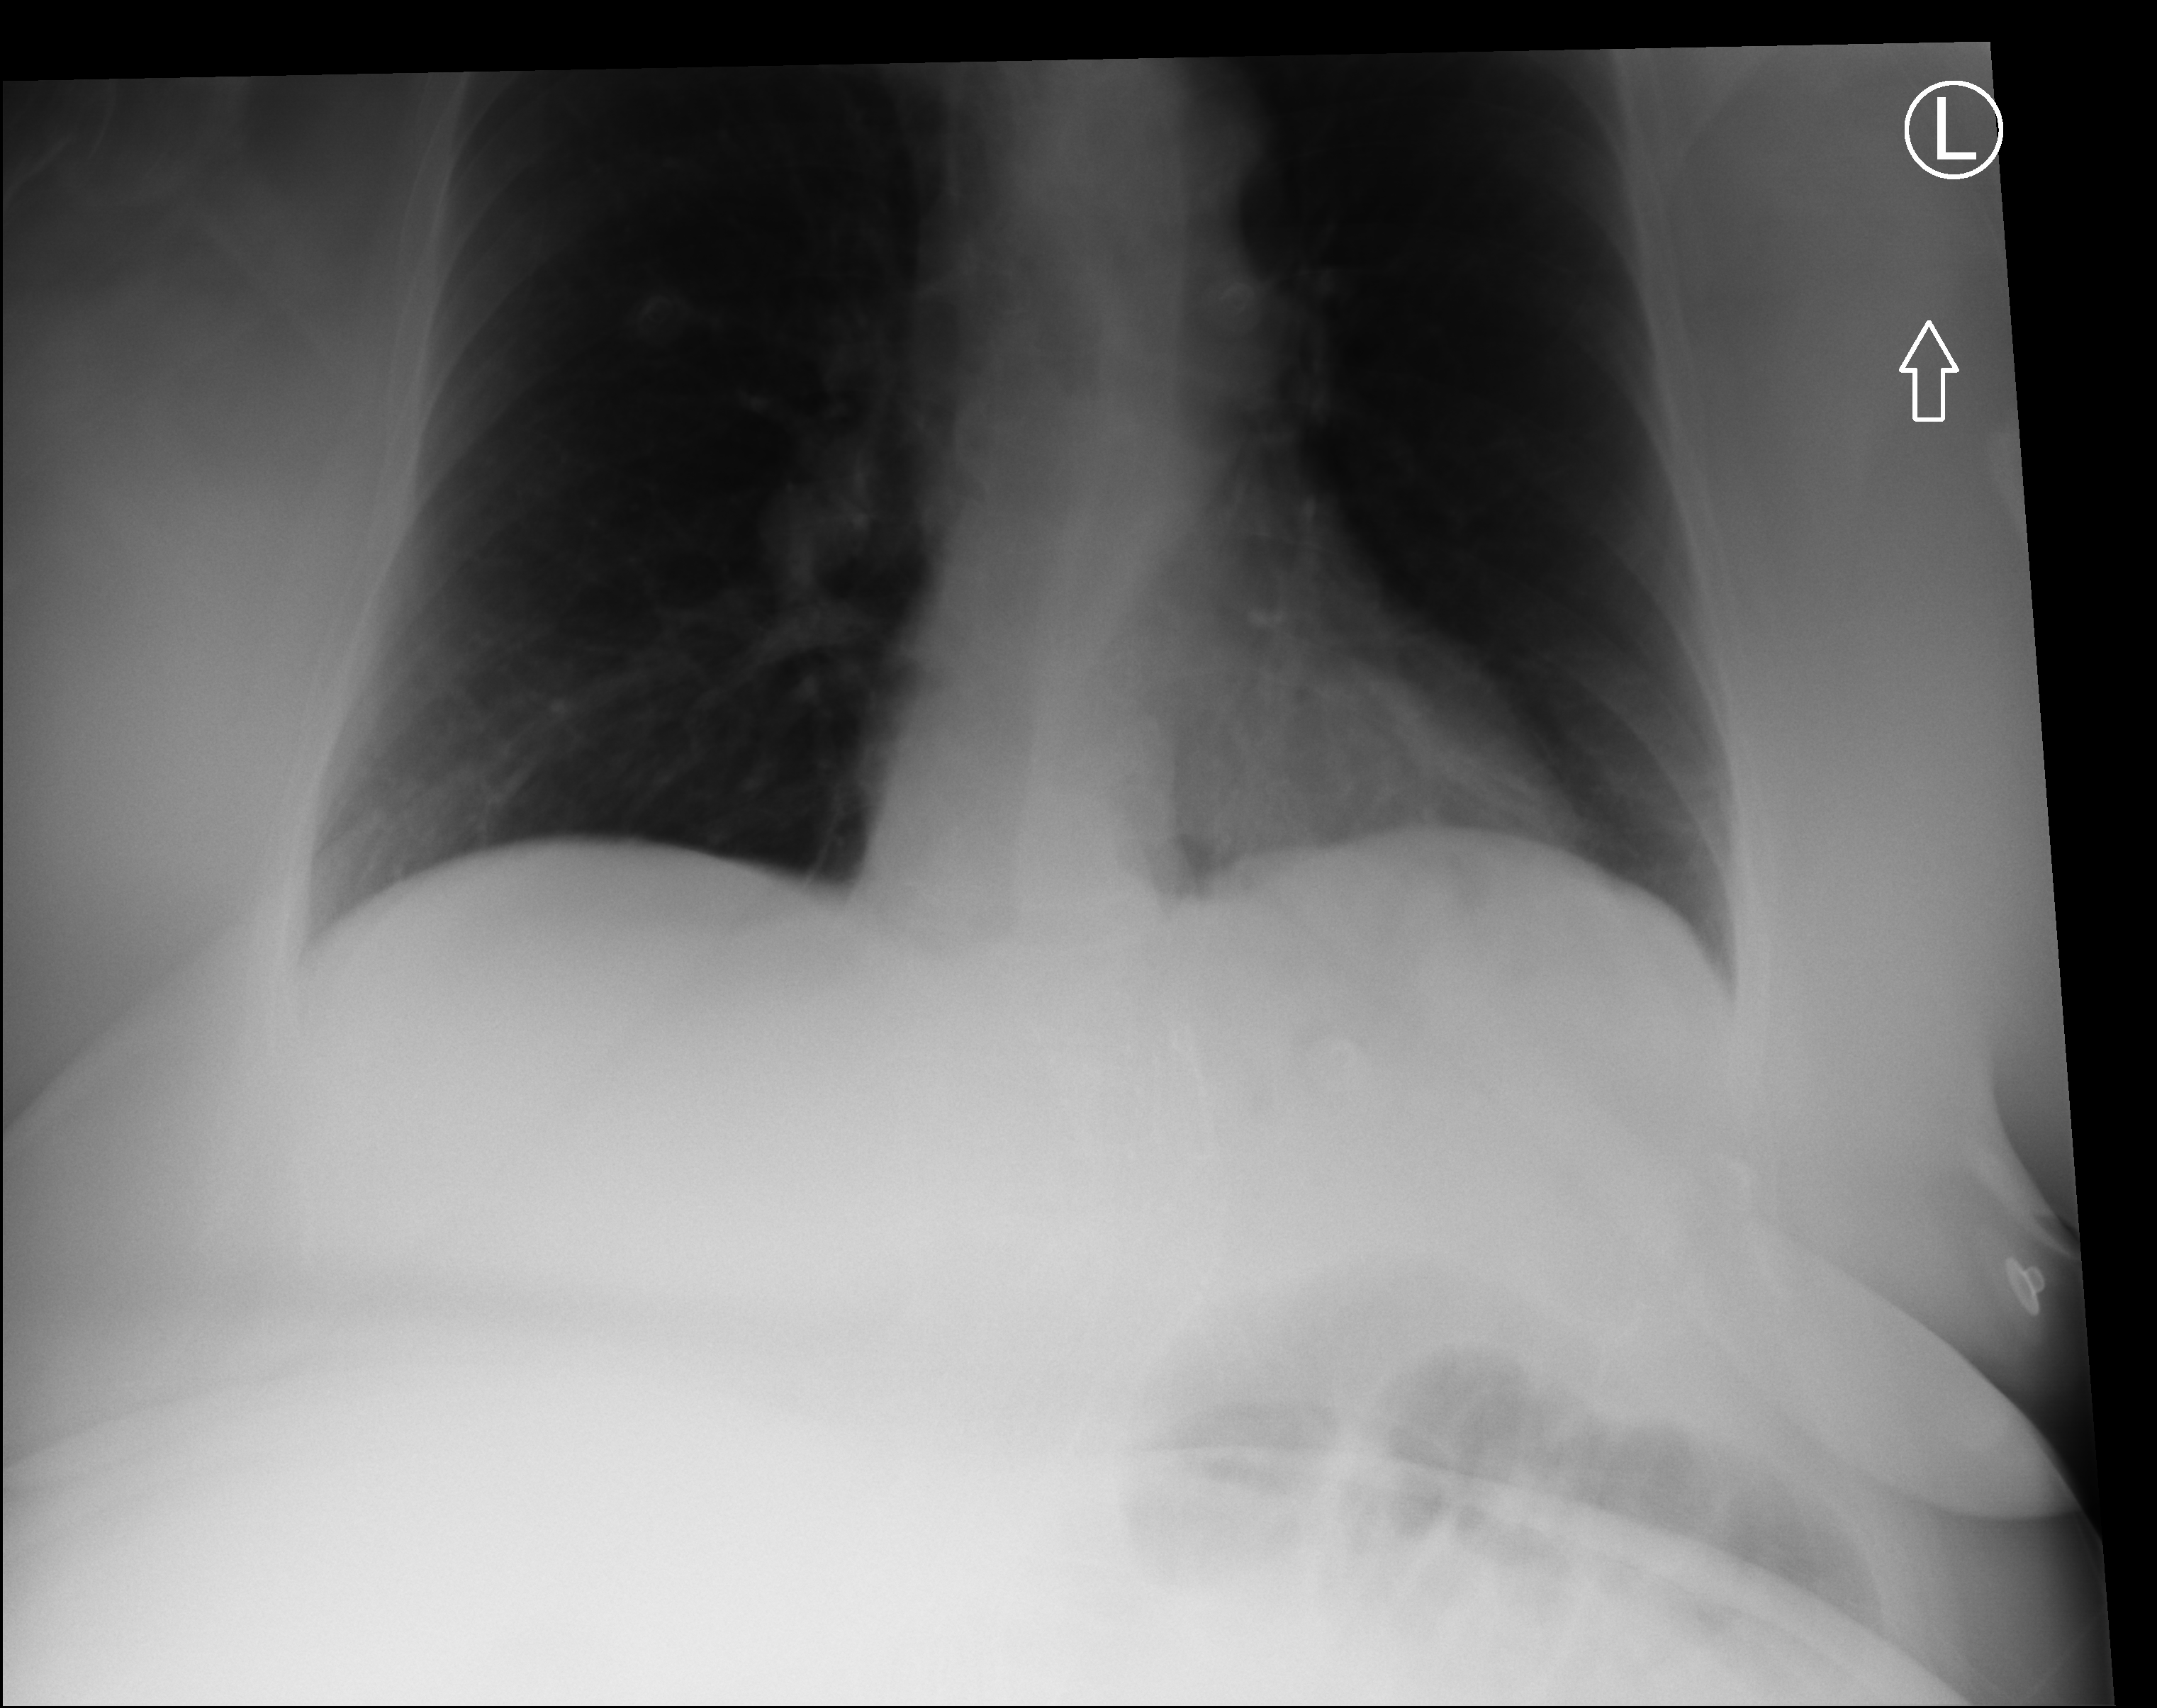
Bedside abdomen radiograph (computed radiography); anteroposterior (AP) projection. Female patient hospitalised with COVID-19, age 60–74 years.
Hospital-stay facts (about this admission, not read from this image; timing relative to this image not recorded): admitted to intensive care during this hospital stay: yes.